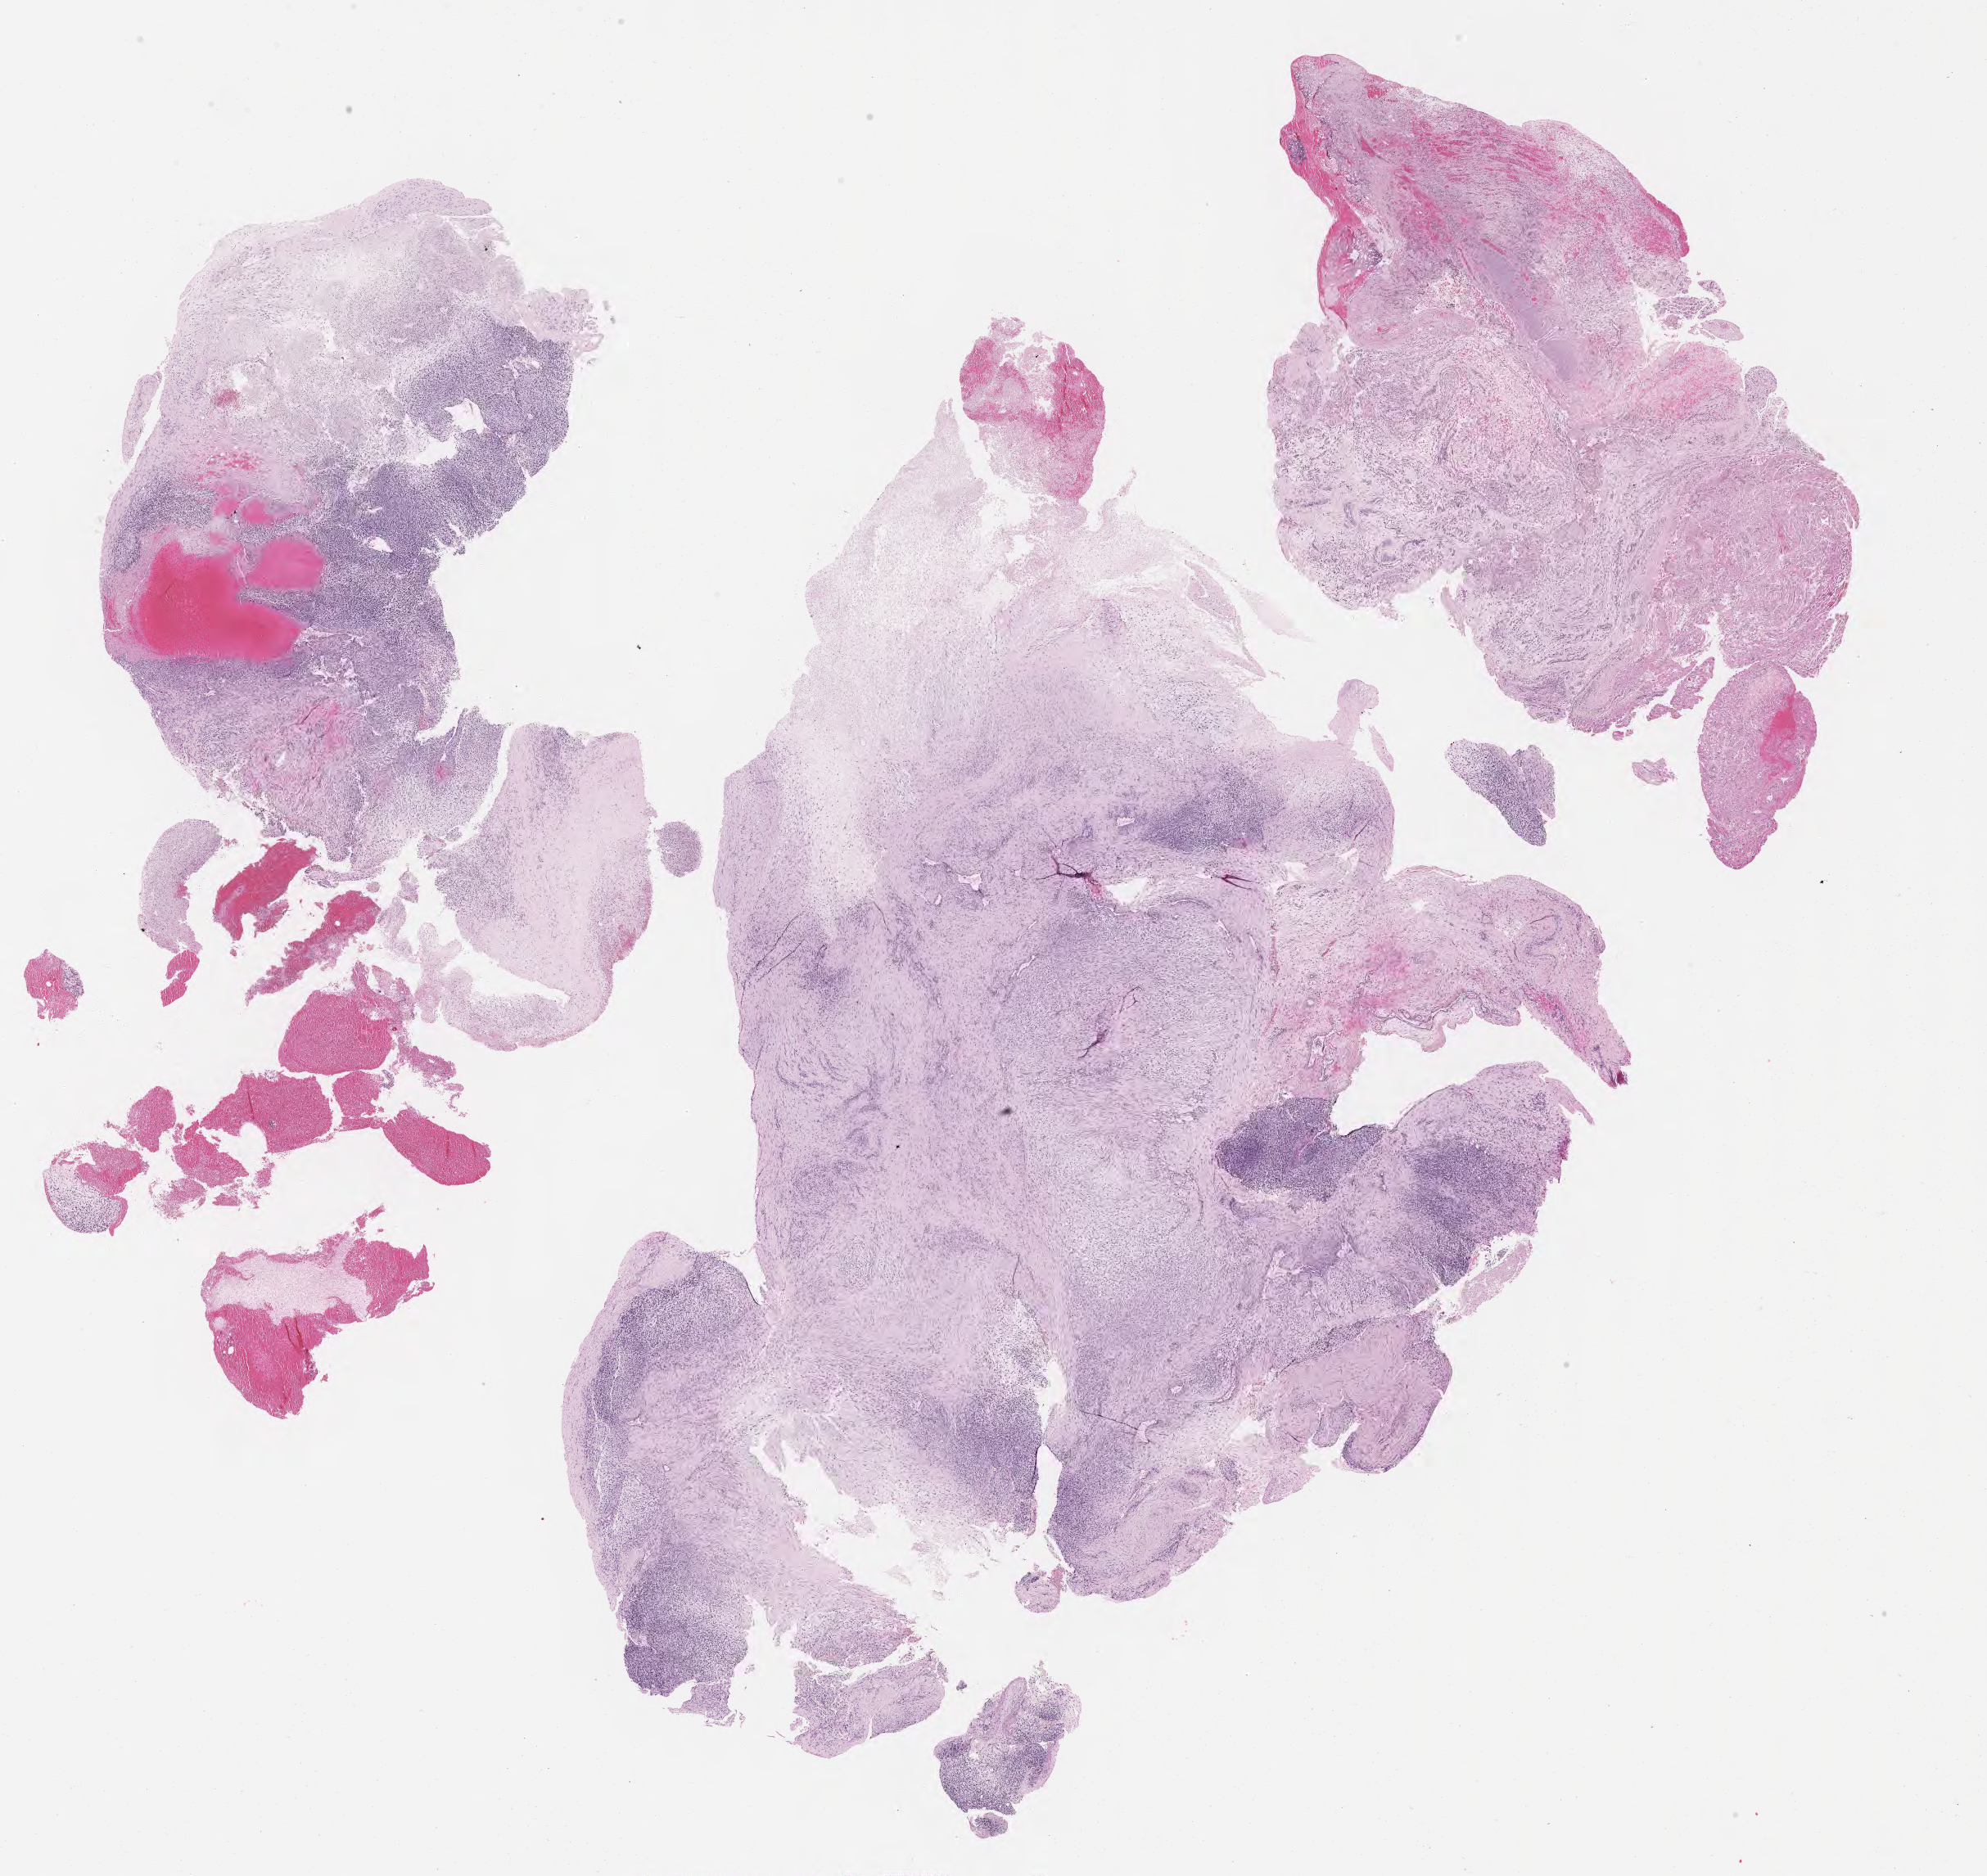
Hematoxylin and eosin (H&E) whole-slide image of tumor tissue, a low-resolution overview of the entire scanned area, about 19.6 x 18.5 mm, formalin-fixed, paraffin-embedded (FFPE) tissue, site: soft tissue - neck, right. Patient: male, age 4.9 years at diagnosis.
Metastatic status at presentation (as recorded): metastatic. Stage (as recorded): 4. Diagnosis: rhabdomyosarcoma; histological classification: embryonal rhabdomyosarcoma.